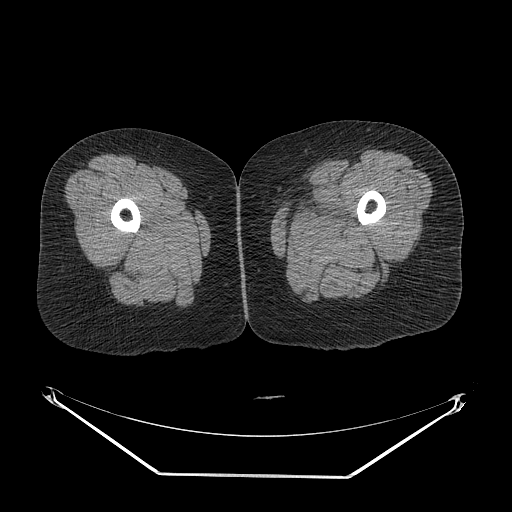
CT of an extremity soft-tissue mass (from a PET/CT study), one axial slice; slice 8 of 267 in the series (ordered by position); reconstruction kernel STANDARD; soft-tissue window (W 400 / L 40 HU); 3.75 mm slice thickness; 512 × 512 image matrix, field of view 500 × 500 mm. Female patient. Case-level facts recorded for this patient, not image findings: histological type: myxofibrosarcoma; grade: intermediate; site of the primary tumour: left thigh.
Structures marked on this image (expert contour drawn on MRI and transferred to this co-registered scan by the dataset authors):
- gross tumour volume including surrounding oedema: bounding box (x1, y1, x2, y2) in pixels: (283, 196, 350, 236)